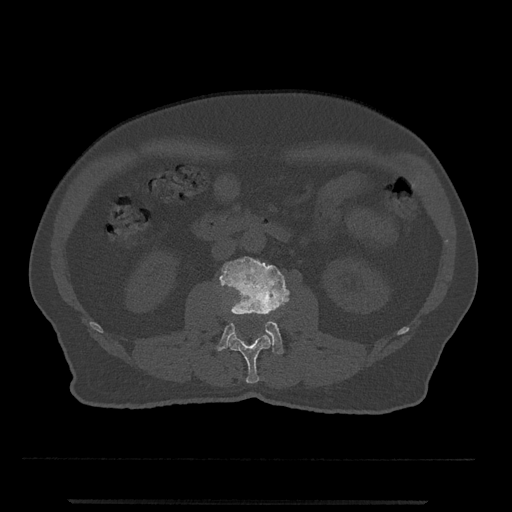
CT including the spine, one axial slice; position 235 of 797 along the scan axis; reconstruction kernel Br40s/3; 120 kVp; bone window (W 1800 / L 400 HU); 0.5 mm slice thickness; 512 × 512 image matrix, field of view 419 × 419 mm. Male patient, age 63 years. Case-level facts recorded for this patient, not image findings: primary cancer: prostate.
Structures marked on this image (semi-automatic segmentation, software-assisted and operator-edited):
- L2 vertebra: bounding box (x1, y1, x2, y2) in pixels: (228, 332, 271, 383)
- L3 vertebra: (217, 256, 290, 354)